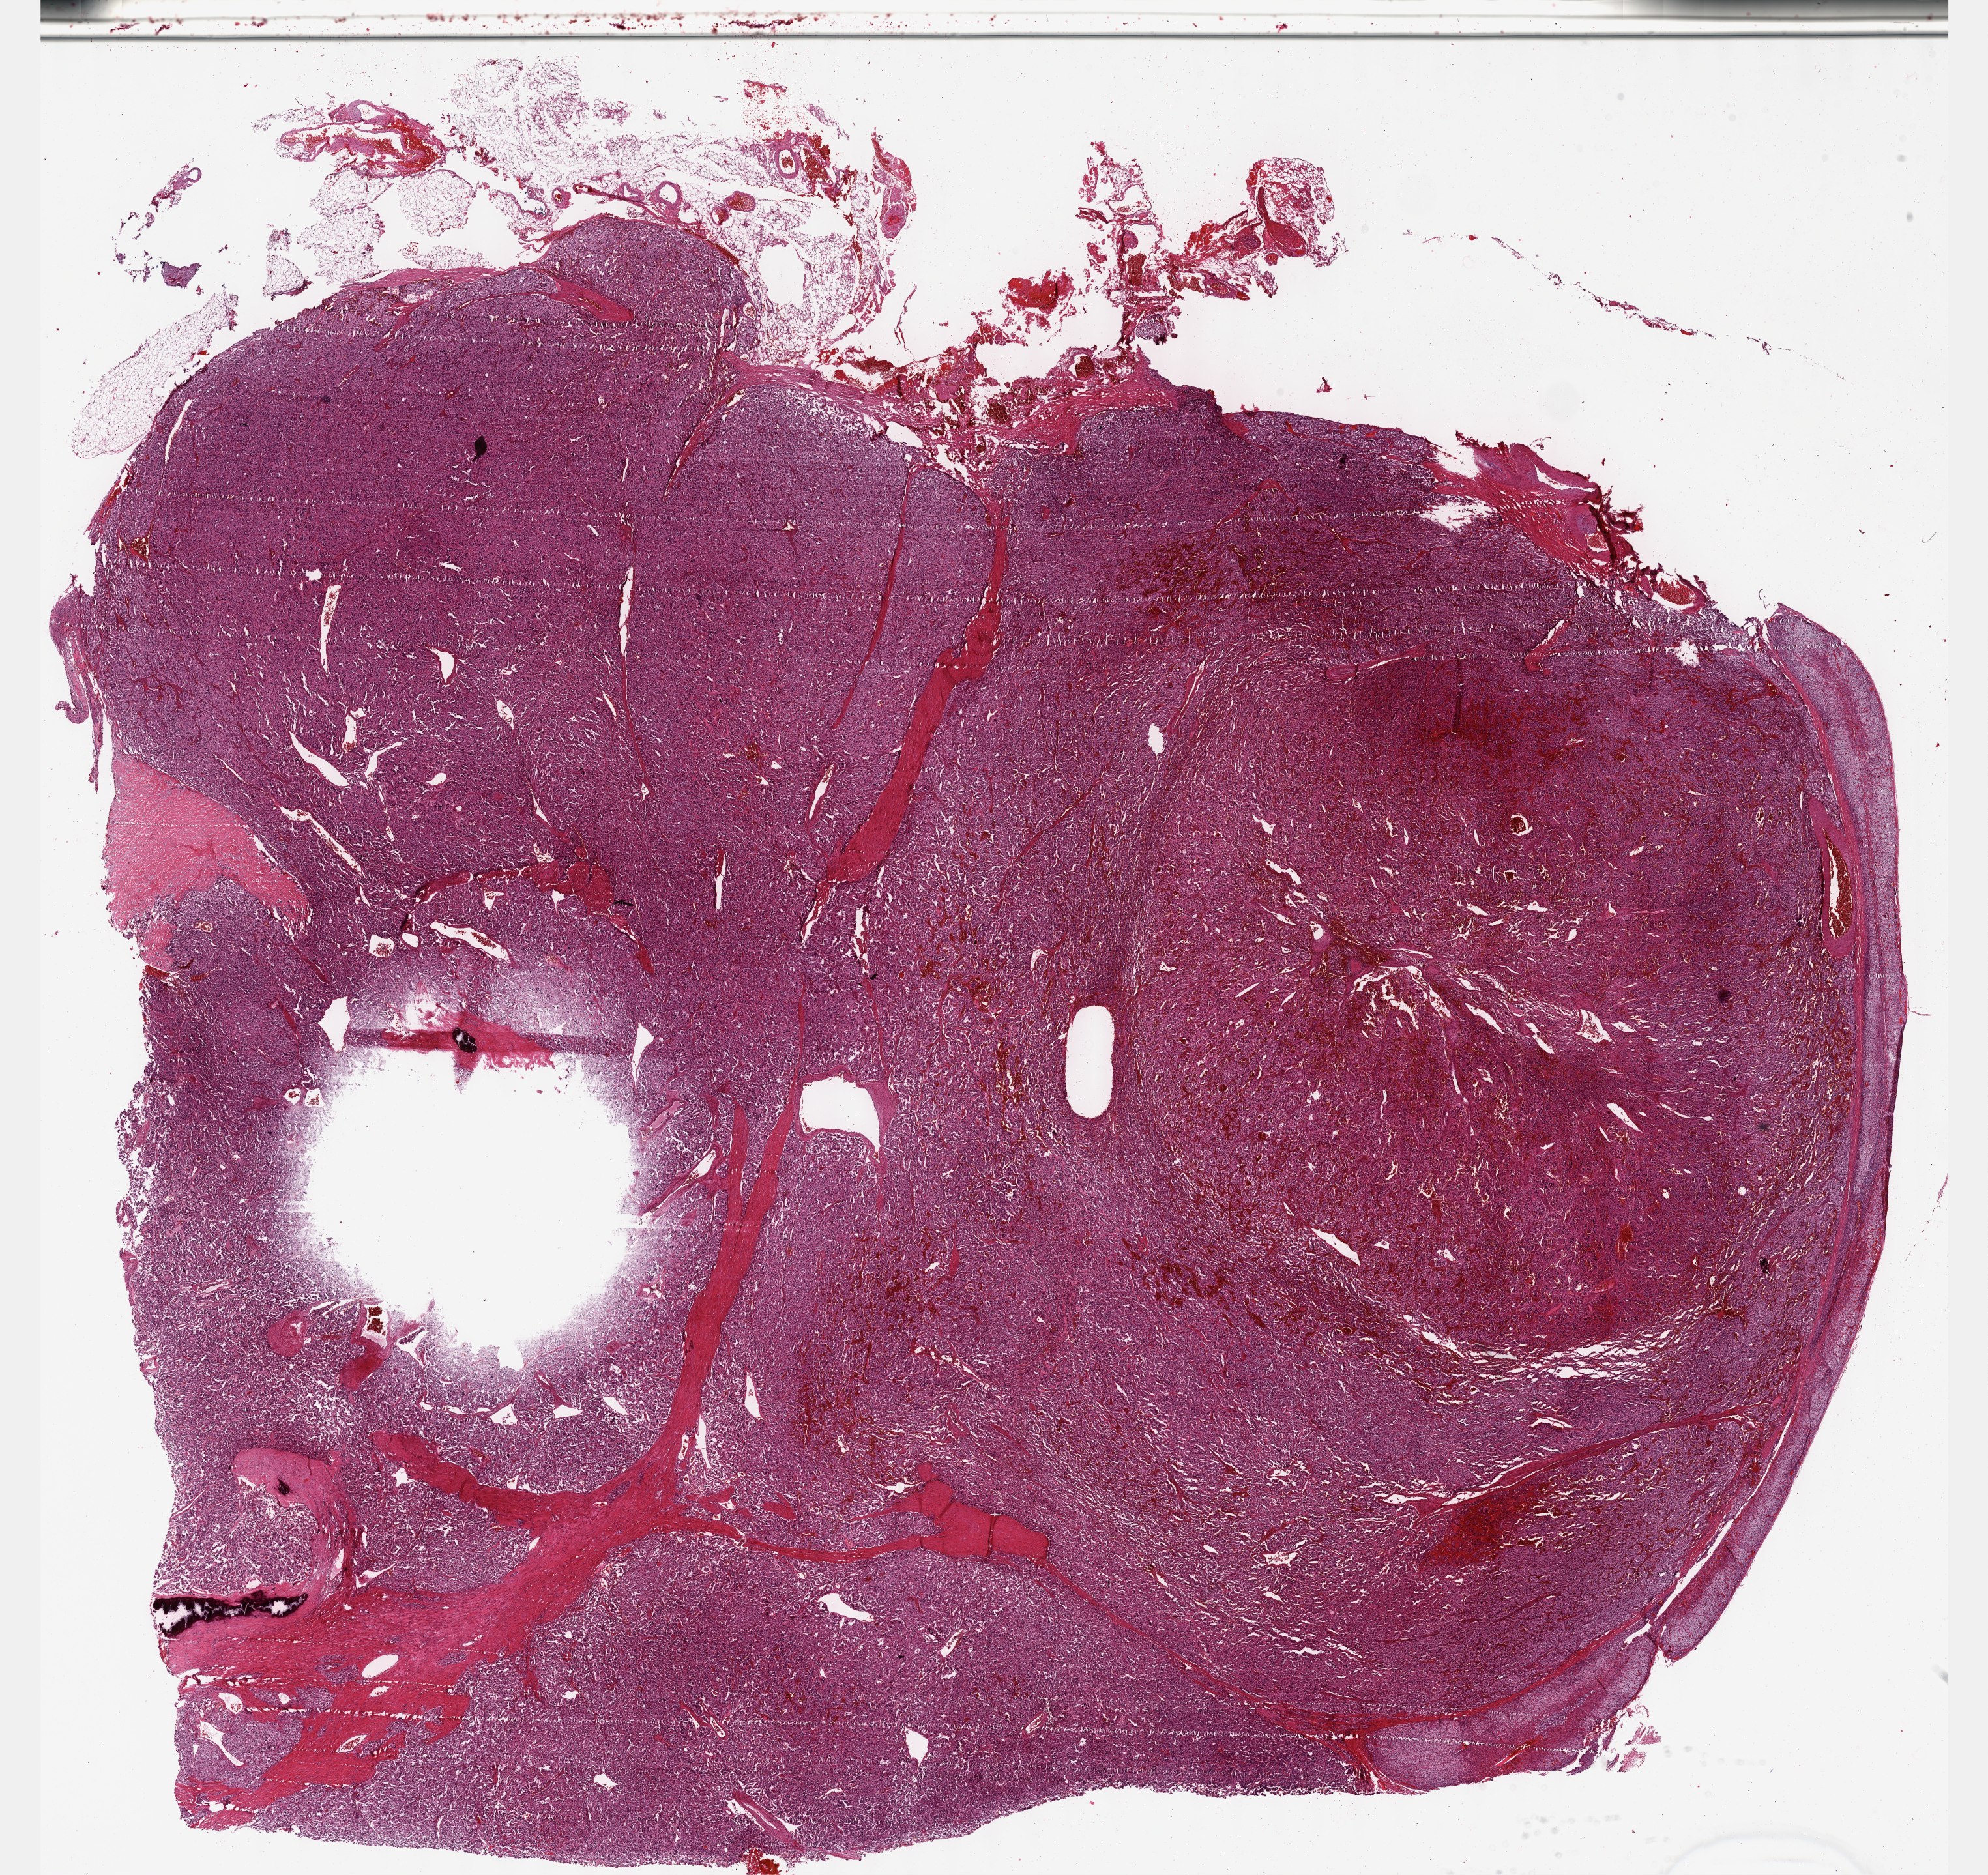
Hematoxylin and eosin (H&E) stained whole-slide image, whole scanned area (about 24.6 x 23.2 mm, slide scanned at 40x) shown as a low-resolution overview; FFPE section; sample: primary tumour, adrenal gland. Male, age 25 years at initial diagnosis.
• histologic diagnosis: Pheochromocytoma, NOS